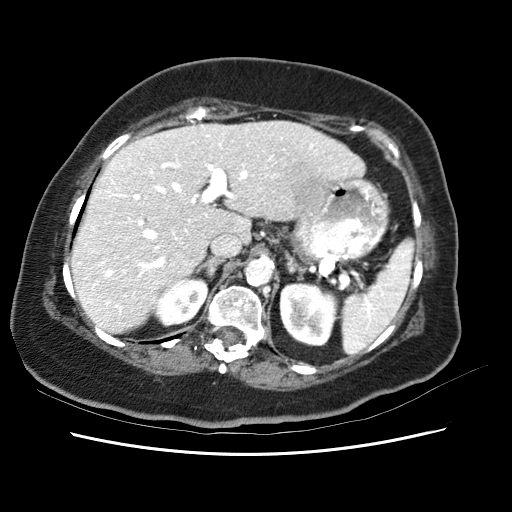
Contrast-enhanced abdominal CT (liver protocol), one axial slice; slice 41 of 62 in the series (ordered by position); reconstruction kernel STANDARD; soft-tissue window (W 400 / L 40 HU); 512 × 512 image matrix. From the clinical record (not read from this slice): diagnosis: hepatocellular carcinoma (patient treated with transarterial chemoembolisation; whether this scan precedes or follows treatment is not stated here); TNM stage (as recorded): Stage-I; Child-Pugh class: B; tumour nodularity: uninodular; tumour size: 5.3 cm.
Structures marked on this image (semi-automatic segmentation, software-assisted and operator-edited):
- liver parenchyma outside the tumour (the mass and vessels are separate outlines, so this box may not span the whole liver): box from (x=72, y=120) to (x=360, y=332) px
- mass: (x=261, y=147)–(x=325, y=221)
- liver vessels: (x=81, y=131)–(x=334, y=306)